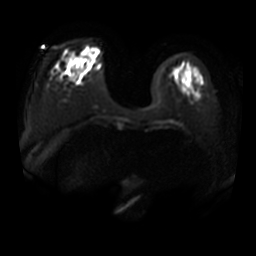
Breast MRI, one axial slice; slice 9 of 34 in the series (ordered by position); diffusion-weighted series; image 2 of 4 stored at this slice position (different b-values; order by instance number); 3 T; 256 × 256 image matrix. Female patient.
Outlined on this slice (outlined manually by an expert reader):
- tumour on diffusion-weighted imaging: bounding box <81,52,85,64> (left, top, right, bottom; pixels)